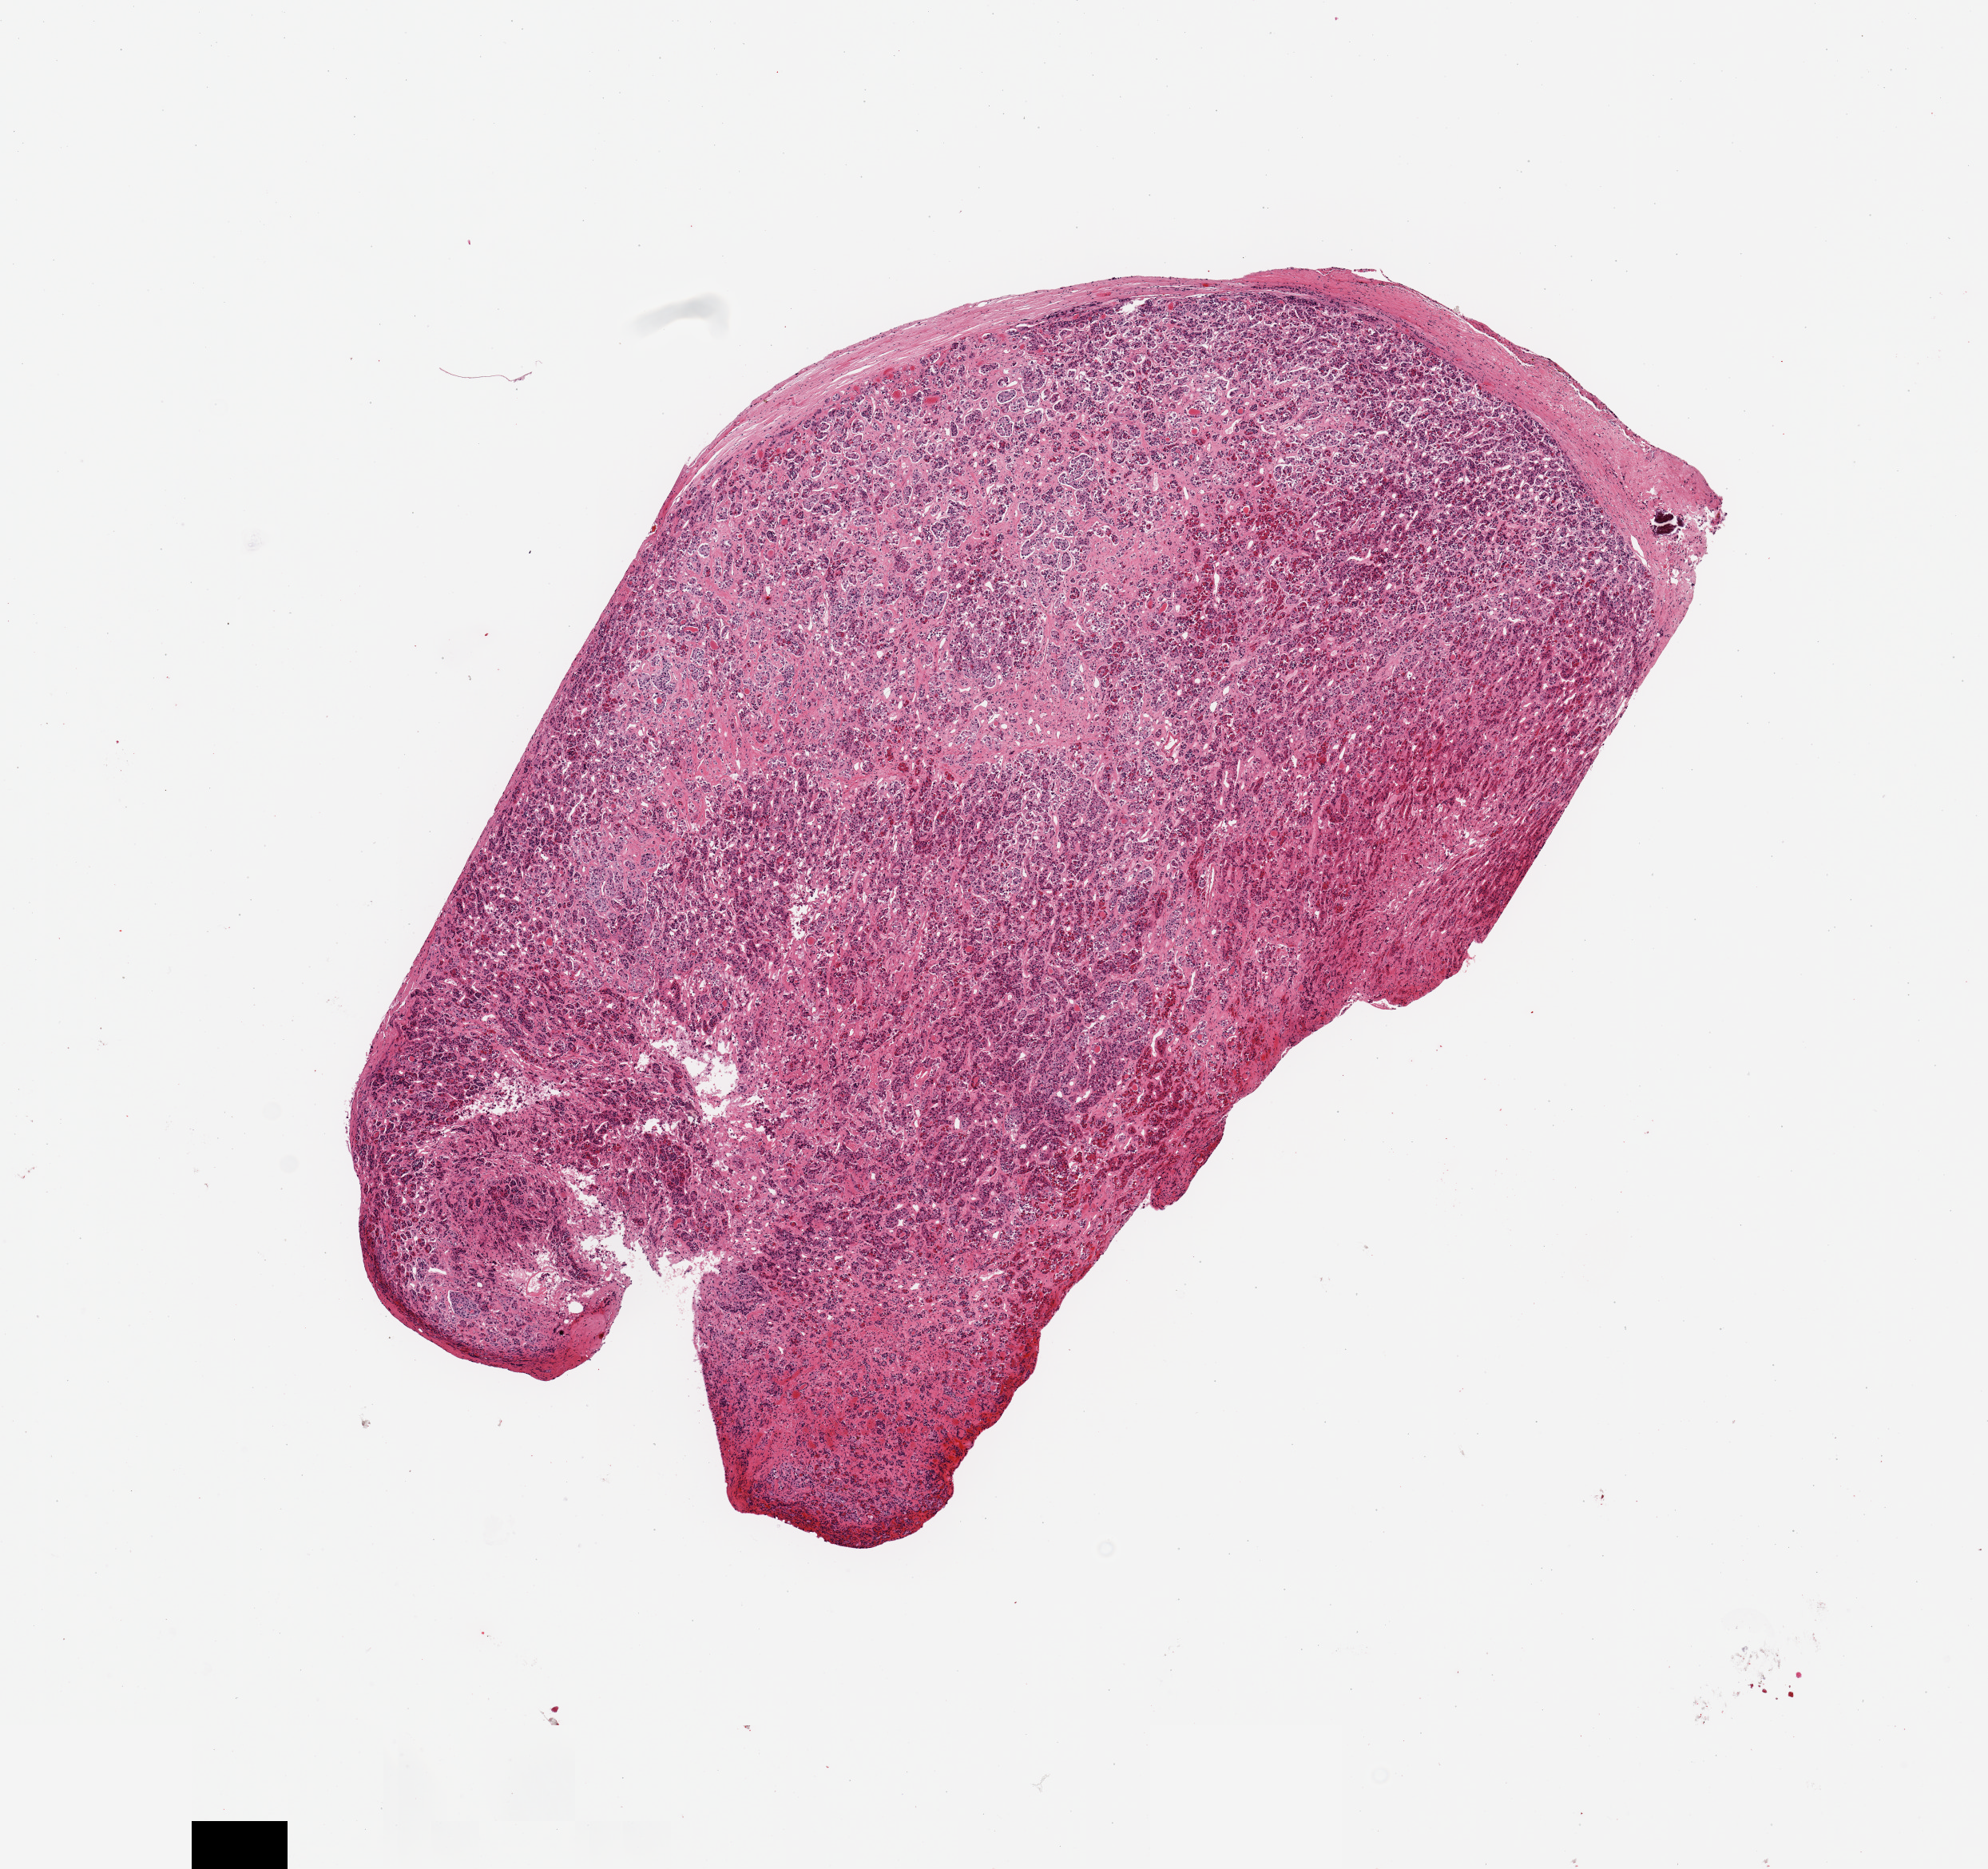
Digitized H&E-stained section, brightfield — a low-resolution overview of the entire scanned area, about 9.8 x 9.3 mm (slide scanned at 20x). PAXgene-fixed, paraffin-embedded tissue. Sampled site (target tissue): pituitary. Tissue donor sample. Male donor.
Reviewer comment on this tissue sample: 1 piece; anterior lobe; patchy interstitial fibrosis.